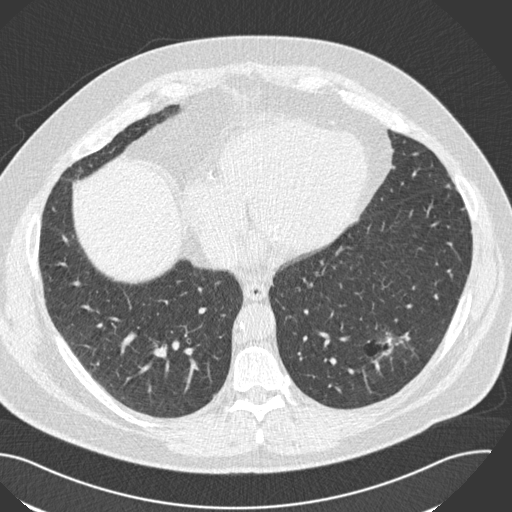
Low-dose screening chest CT, axial slice. Third screening round (two years after baseline). Lung window (W 1500 / L -600 HU). 2 mm slice thickness. Standard (soft-tissue) reconstruction kernel (B30f). Slice 90 of 153 in the series. 512 × 512 image matrix. Male, age 57 years at enrolment. Current smoker at enrolment.
- Expert reader's lesion annotation, bounding box (x1, y1, x2, y2) in pixels: (349, 319, 425, 380).
- The exam's reader record, not a measurement of the box and not confirmed to be the same lesion: non-calcified nodule or mass ≥4 mm, left lower lobe, 22 × 18 mm, poorly defined margins, soft tissue attenuation, pre-existing on the prior screen: yes; interval growth: yes.
- Participant outcome: lung cancer diagnosed 124 days after this screen — squamous cell carcinoma, NOS, left lower lobe, moderately differentiated (G2), stage IA (AJCC 6th edition), 22 mm at pathology.